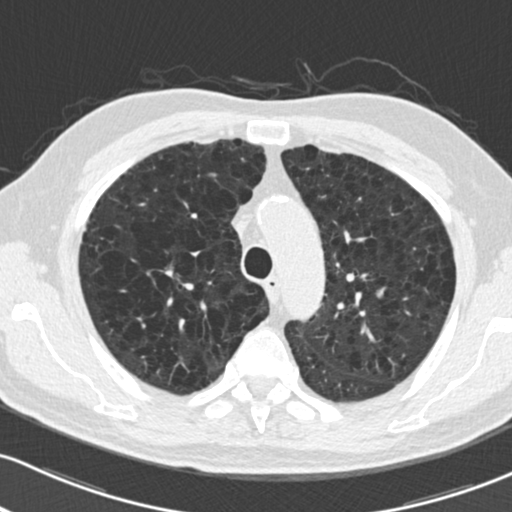
Axial slice from a low-dose chest CT screening exam, second annual screen, lung window (W 1500 / L -600 HU), 2 mm slice thickness. Male, age 73 years at enrolment. Current smoker at enrolment.
Expert-annotated lung lesion, bounding box <151,255,191,288> (left, top, right, bottom; pixels). Reader record for this screening exam (exam-level; its link to the box is not recorded): non-calcified nodule or mass ≥4 mm, right upper lobe, 10 × 9 mm, smooth margins, soft tissue attenuation, pre-existing on the prior screen: yes; interval growth: yes. Participant outcome: lung cancer diagnosed 51 days after this screen — squamous cell carcinoma, NOS, right upper lobe, stage IA (AJCC 6th edition), 10 mm at pathology.